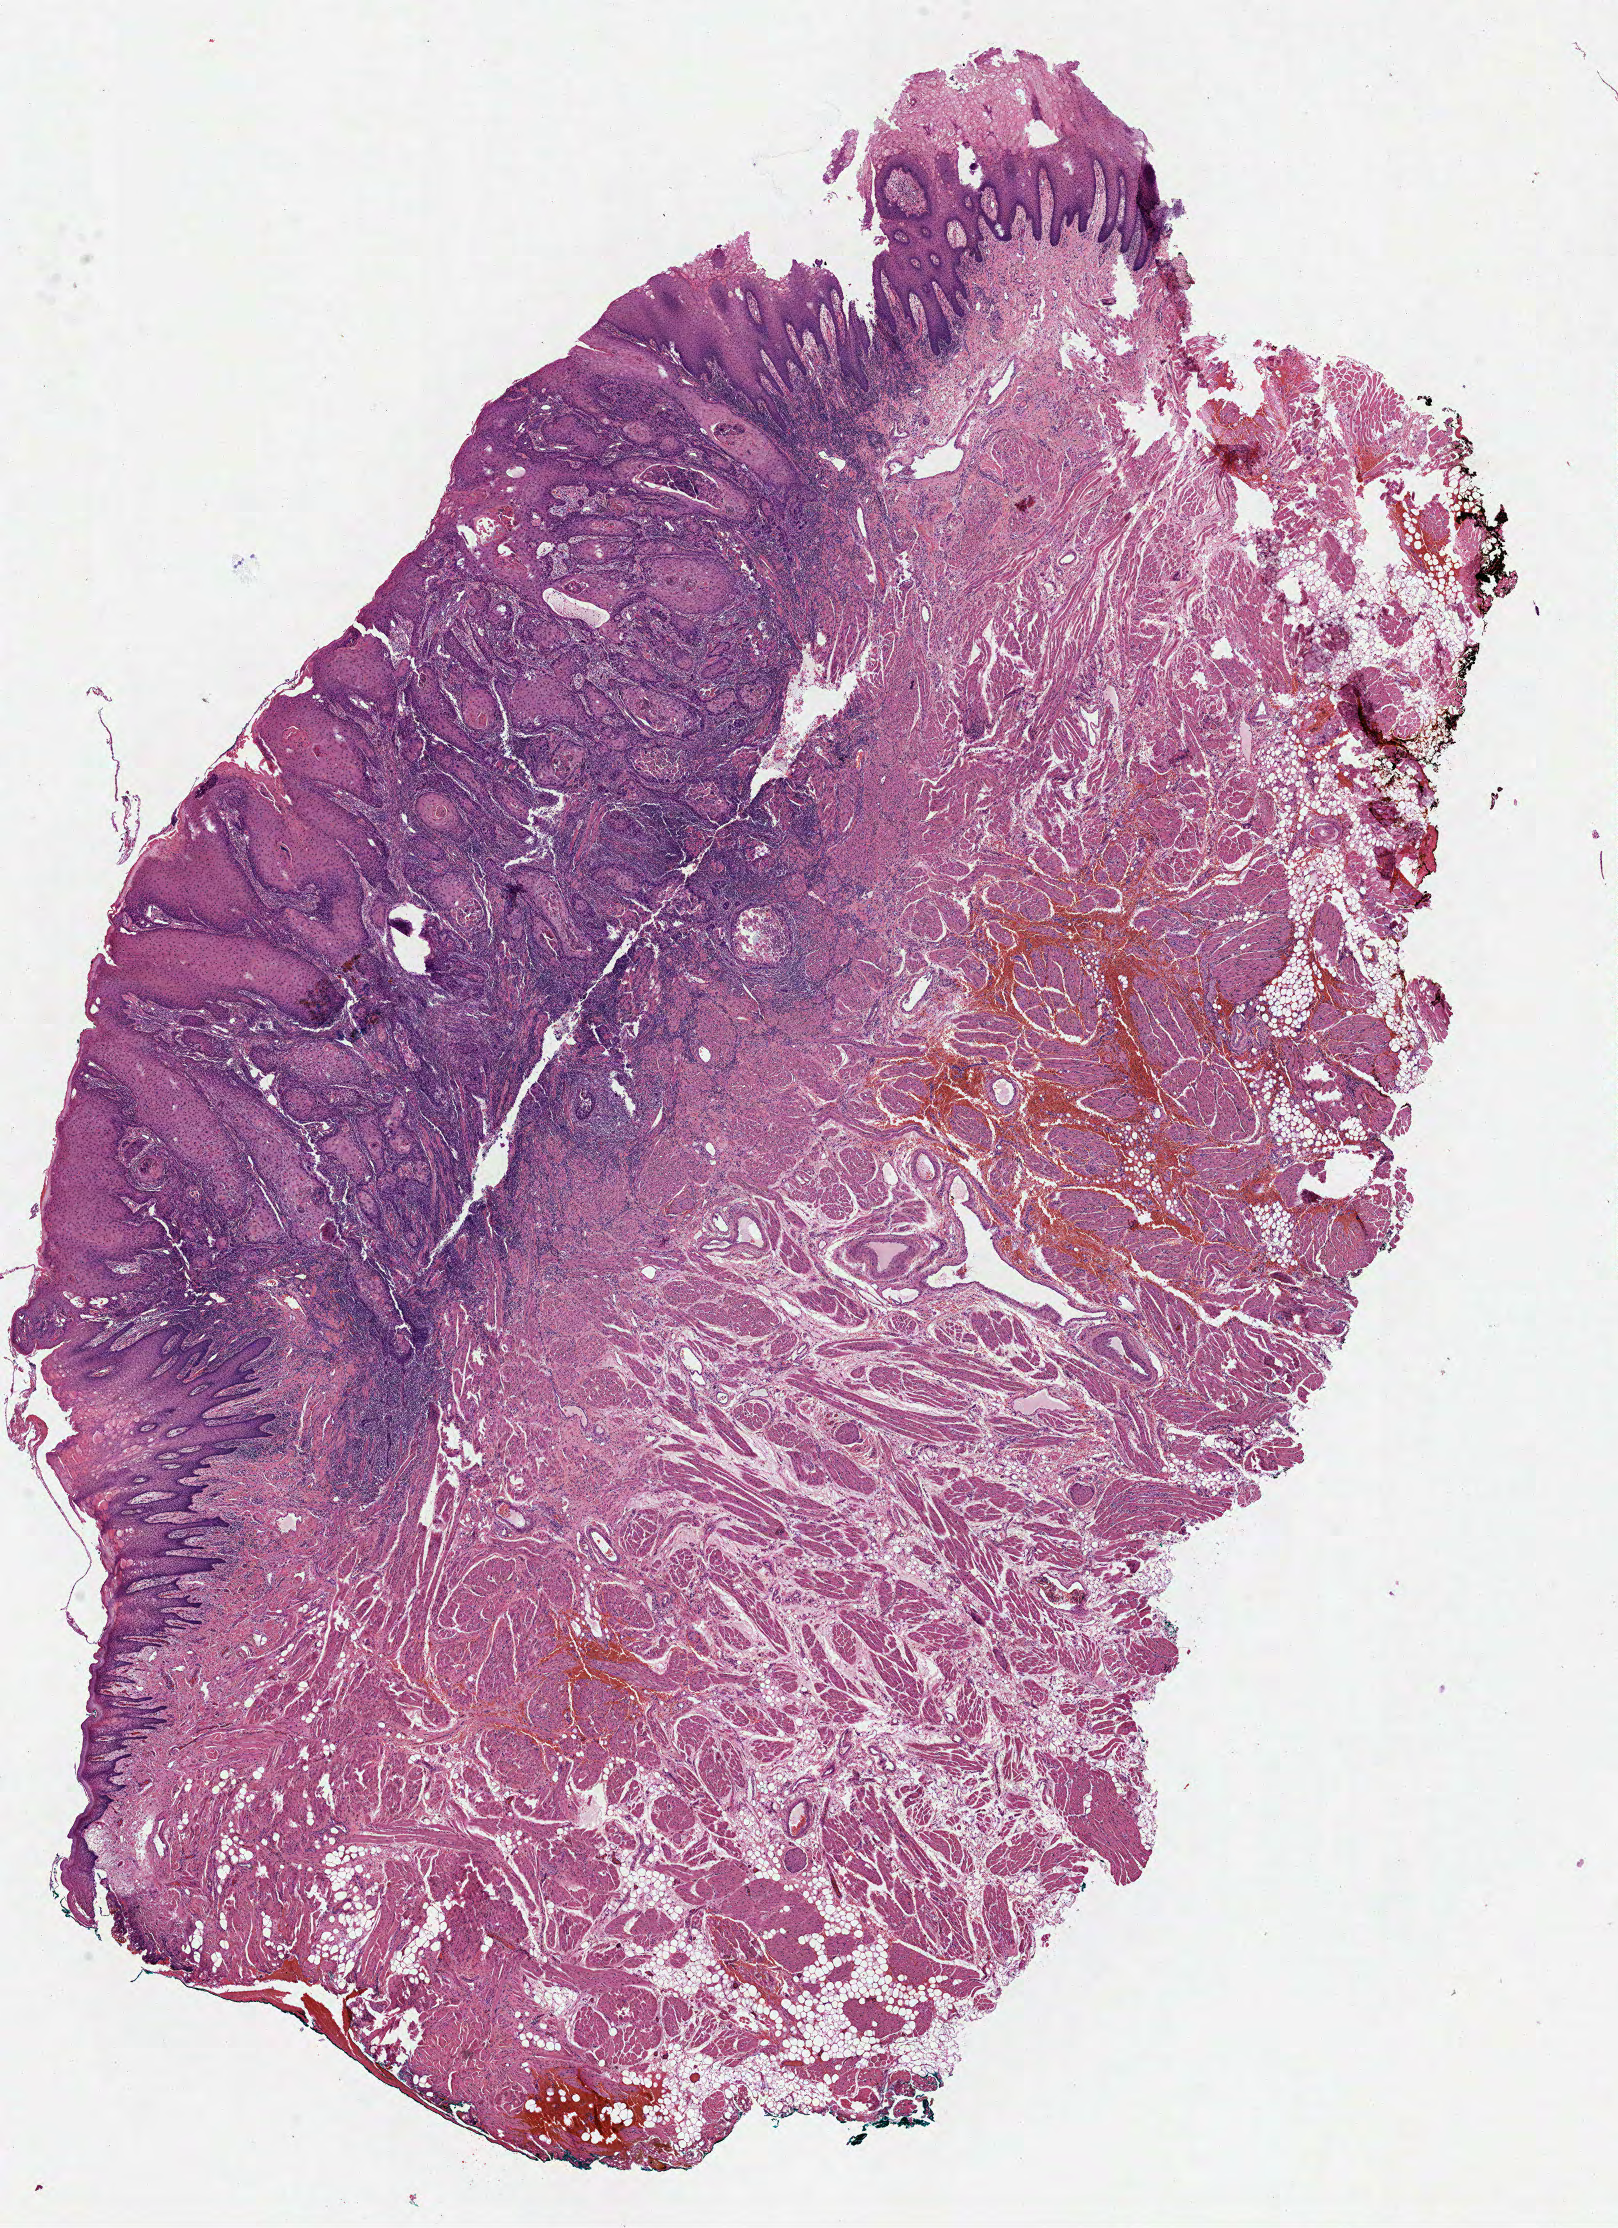
H&E-stained whole-slide image — whole scanned area (about 13.1 x 18.0 mm, acquisition: 40x scan) shown as a low-resolution overview; formalin-fixed paraffin-embedded (FFPE) diagnostic section; head and neck, primary tumour sample. Female, age 51 years at initial diagnosis.
Diagnosis: Squamous cell carcinoma, NOS (tongue, NOS).